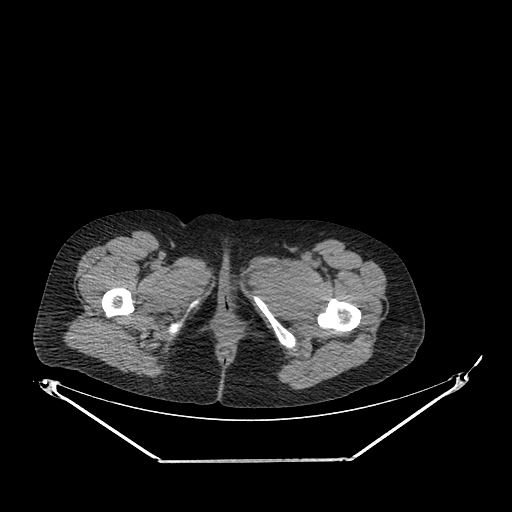
CT of an extremity soft-tissue mass (from a PET/CT study), one axial slice. 120 kVp. Soft-tissue window (W 400 / L 40 HU). 512 × 512 image matrix. Female patient. From the clinical record (not read from this slice): histological type: pleiomorphic leiomyosarcoma; grade: intermediate; site of the primary tumour: left thigh.
Structures marked on this image (expert contour drawn on MRI and transferred to this co-registered scan by the dataset authors):
- gross tumour volume including surrounding oedema: bounding box <247,260,312,305> (left, top, right, bottom; pixels)
- gross tumour volume (mass): <269,265,309,303>